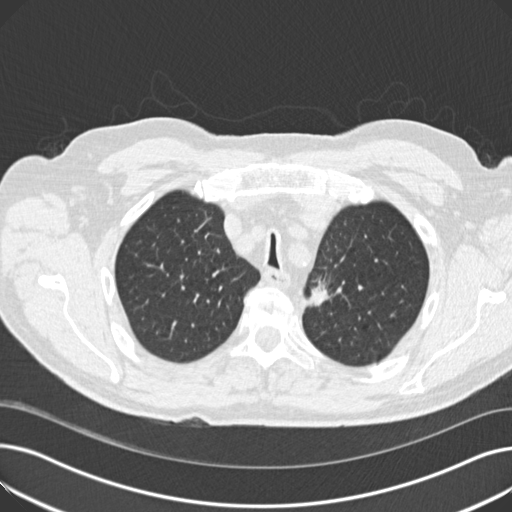
Axial slice from a low-dose chest CT screening exam. Third annual screen. Lung window (W 1500 / L -600 HU). Slice 45 of 191 in the series. 512 × 512 image matrix. Male, age 70 years at enrolment. Current smoker at enrolment.
- Expert reader's lesion annotation, bounding box <299,271,341,313> (left, top, right, bottom; pixels).
- The screening reader recorded 2 non-calcified nodules or masses ≥4 mm on this exam (left upper lobe, left lower lobe); which of them this box marks is not recorded.
- Official screen result: positive, other.
- Participant outcome: lung cancer diagnosed 175 days after this screen — mixed cell adenocarcinoma, left upper lobe, poorly differentiated (G3), stage IIB (AJCC 6th edition), 17 mm at pathology.